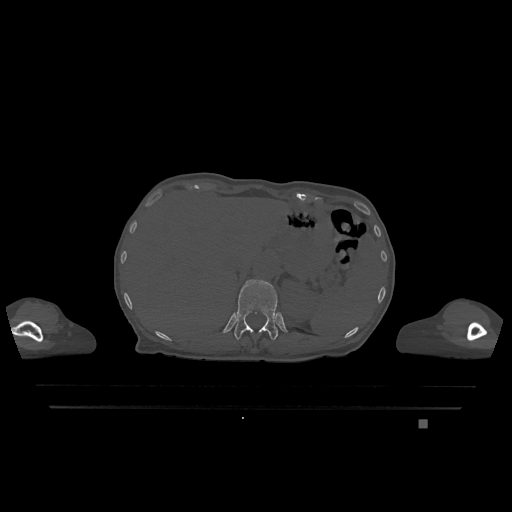
CT including the spine, one axial slice; position 541 of 1317 along the scan axis; bone window (W 1800 / L 400 HU); 512 × 512 image matrix, field of view 500 × 500 mm. Female patient, age 74 years. From the clinical record (not read from this slice): primary cancer: lung.
Structures marked on this image (semi-automatically segmented with operator editing):
- T12 vertebra: bounding box (x1, y1, x2, y2) in pixels: (234, 280, 278, 340)